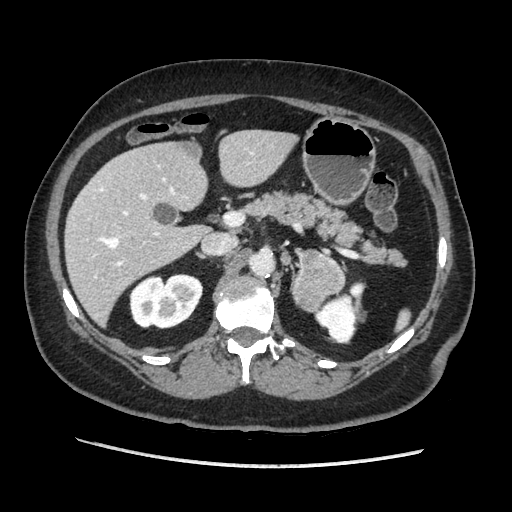
Contrast-enhanced abdominal CT, one axial slice. Slice 116 of 203 in the series (ordered by position). Soft-tissue window (W 400 / L 40 HU). 1.25 mm slice thickness. 512 × 512 image matrix, field of view 360 × 360 mm. Female patient. Case-level facts recorded for this patient, not image findings: diagnosis: adrenocortical carcinoma; tumour side: left adrenal.
Annotated regions visible in this slice (semi-automatic segmentation, software-assisted and operator-edited):
- mass: box from (x=294, y=249) to (x=345, y=311) px